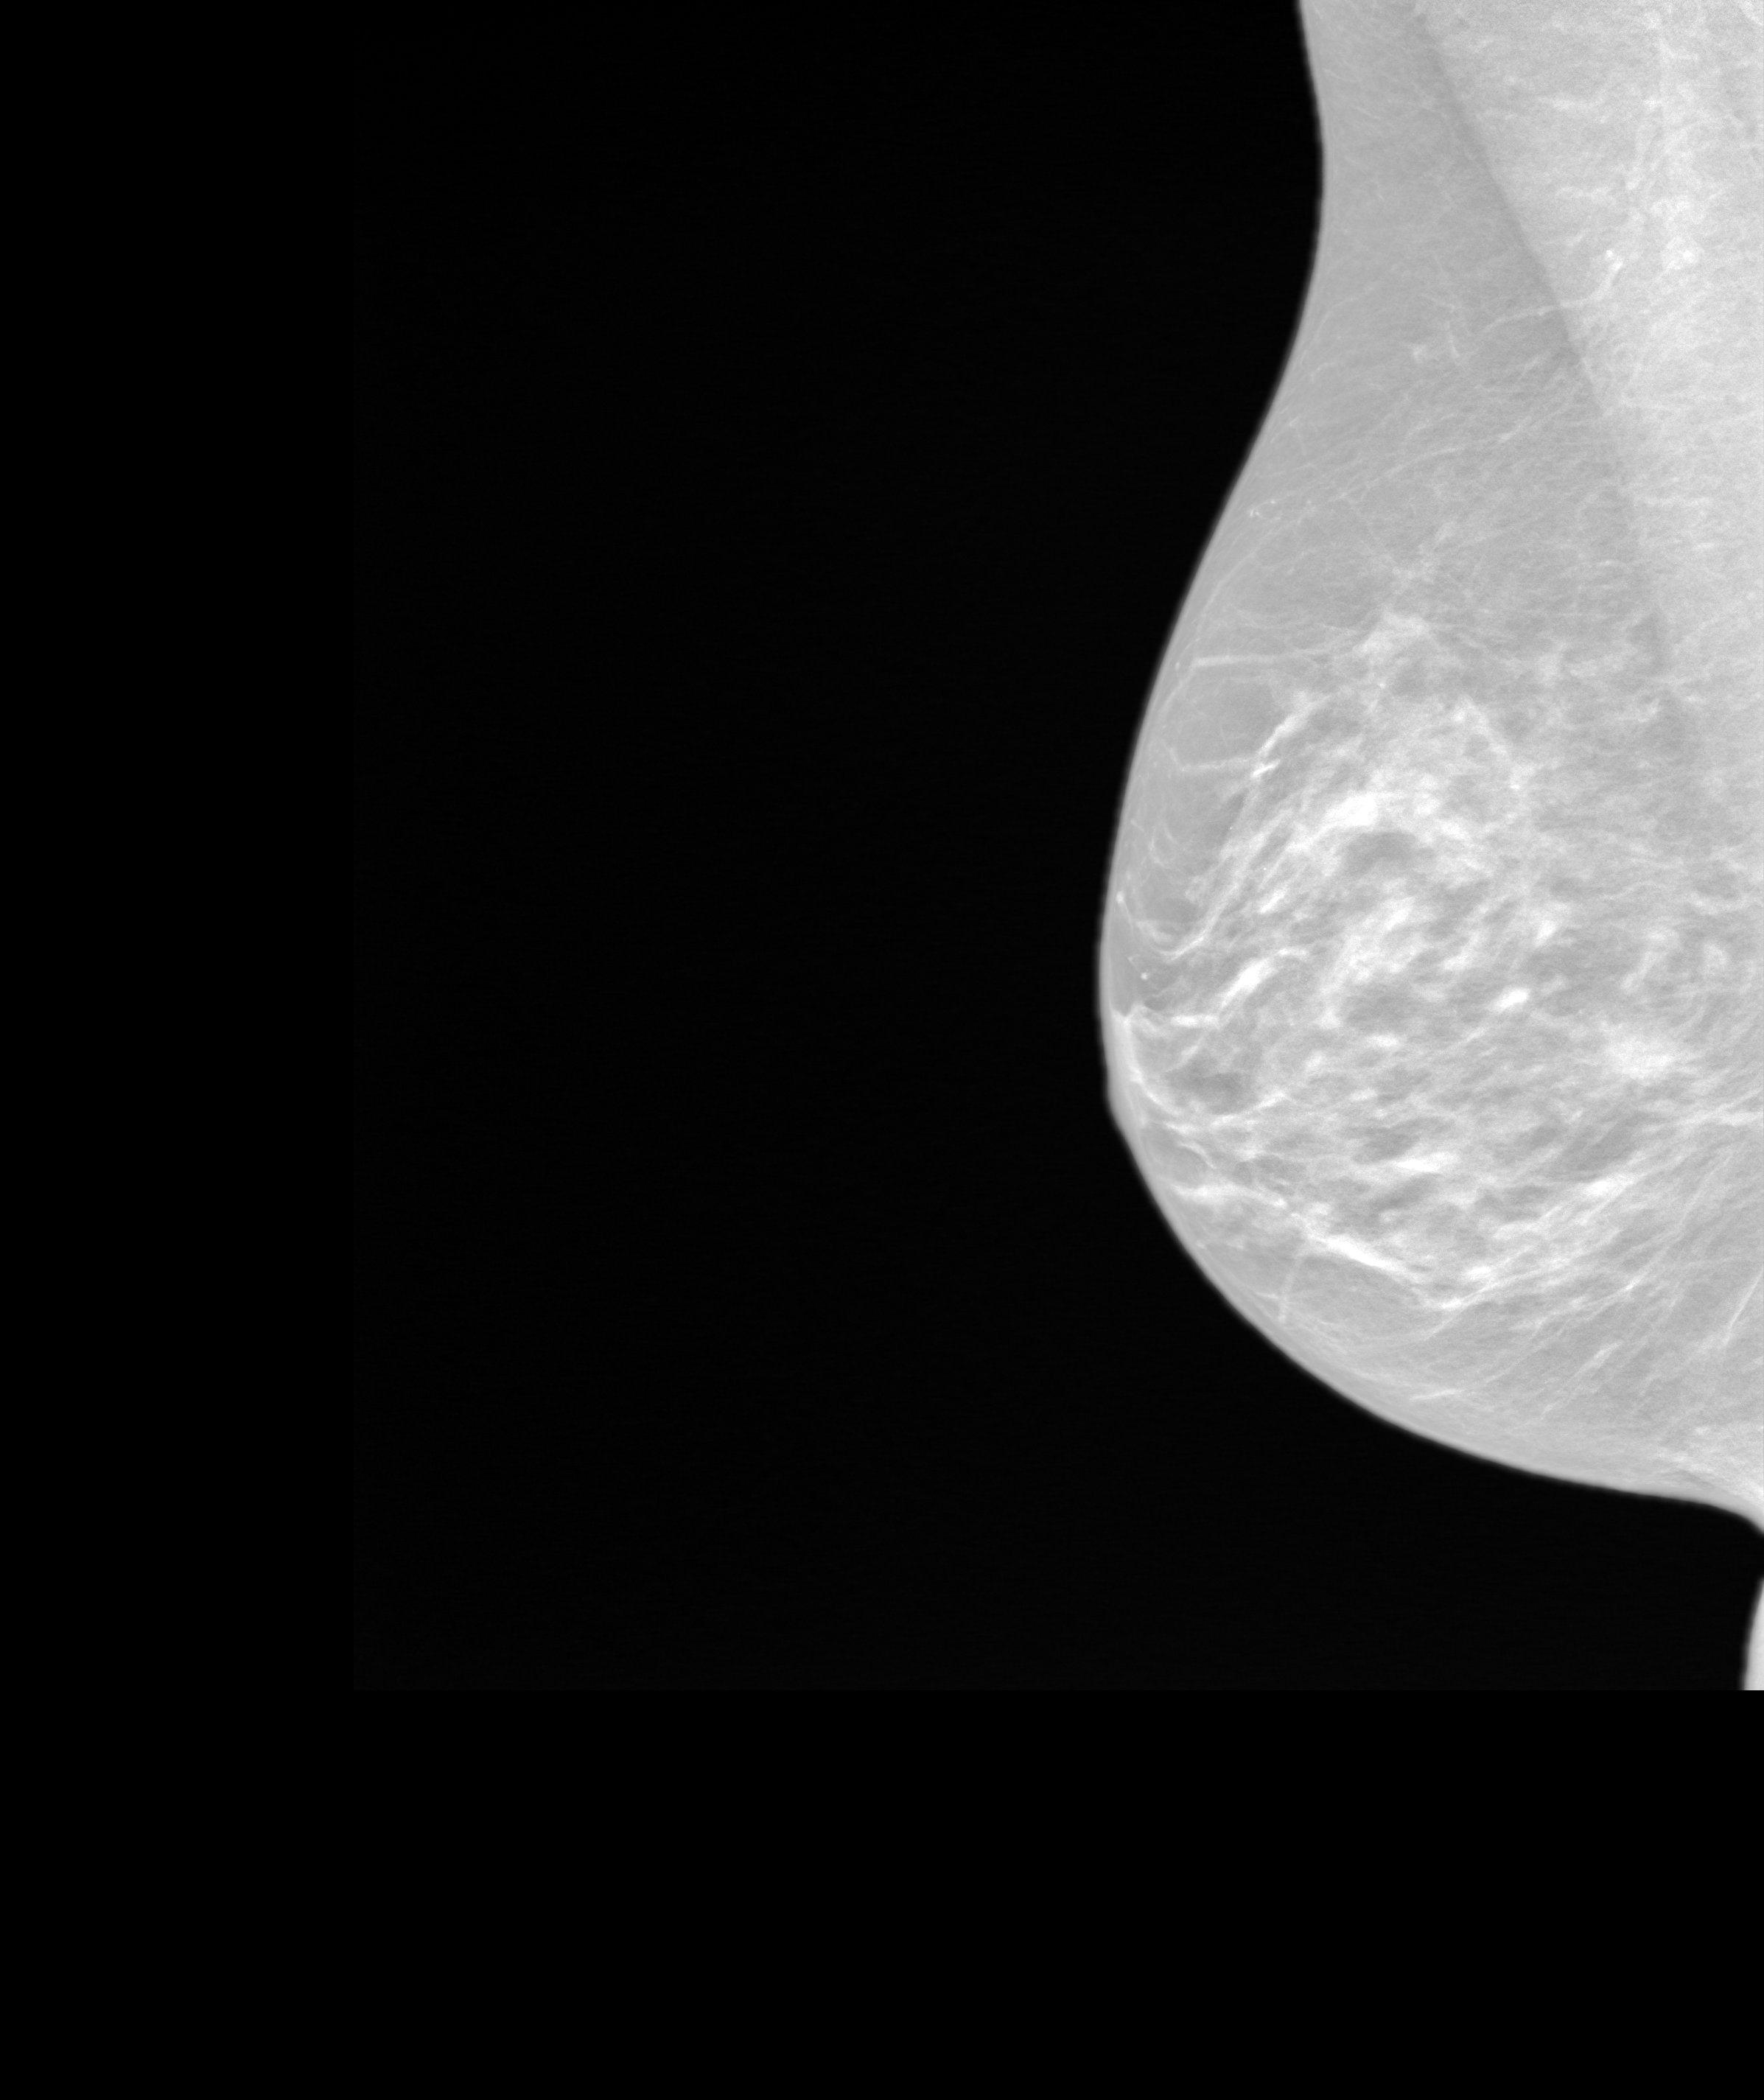
Screening examination. Patient: female, 59 years.
Image type: synthesized 2-D view from tomosynthesis. Breast: right. Projection: MLO view.